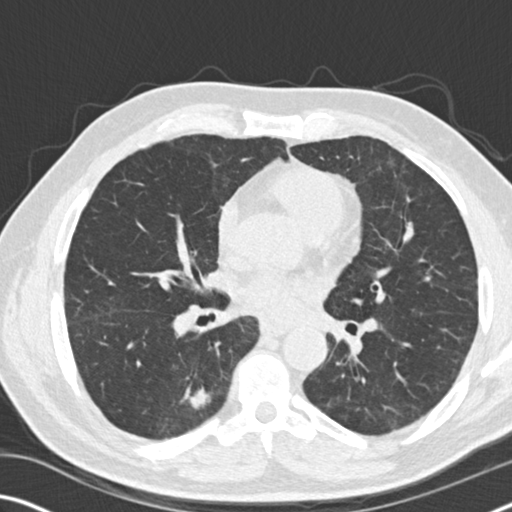
Low-dose screening chest CT, one axial slice. Position 85 of 169 along the scan axis. Reconstruction kernel B30f. Lung window (W 1500 / L -600 HU). 2 mm slice thickness. 512 × 512 image matrix, field of view 340 × 340 mm.
Structures marked on this image (expert manual segmentation):
- lesion 1 (tumor, lower lobe of right lung): bounding box [x1, y1, x2, y2] px = [189, 387, 211, 409]